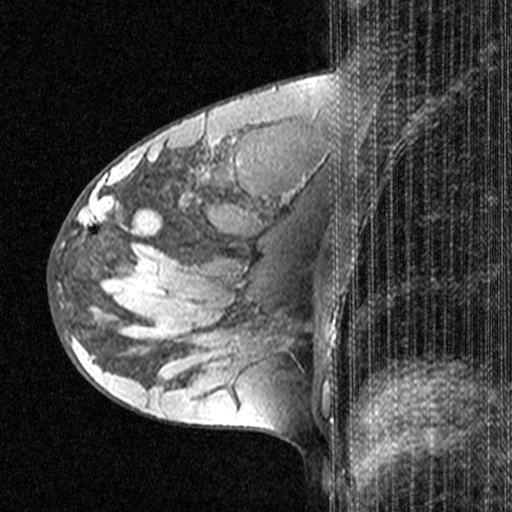
Breast MRI (dynamic contrast-enhanced), one sagittal slice. Slice 20 of 44 in the series (ordered by position). Dynamic contrast-enhanced study with each time point stored as its own series, time point 2 of 3 at this slice position (early post-contrast, ordered by acquisition time). 1.5 T. TE 4.5 ms, TR 11 ms. 3 mm slice thickness. 512 × 512 image matrix, field of view 200 × 200 mm. Female patient, age 28 years. Case-level facts recorded for this patient, not image findings: setting: breast cancer imaged before/during neoadjuvant chemotherapy; receptor status: HR-positive, HER2-negative.
Outlined on this slice (semi-automatic segmentation, software-assisted and operator-edited):
- analysis volume of interest (the breast-tissue region the enhancement analysis was run in; not a lesion): bounding box <48,182,151,283> (left, top, right, bottom; pixels)
- tumour enhancement mask (voxels above the 90 % enhancement threshold inside the analysis volume of interest): <84,182,101,226>